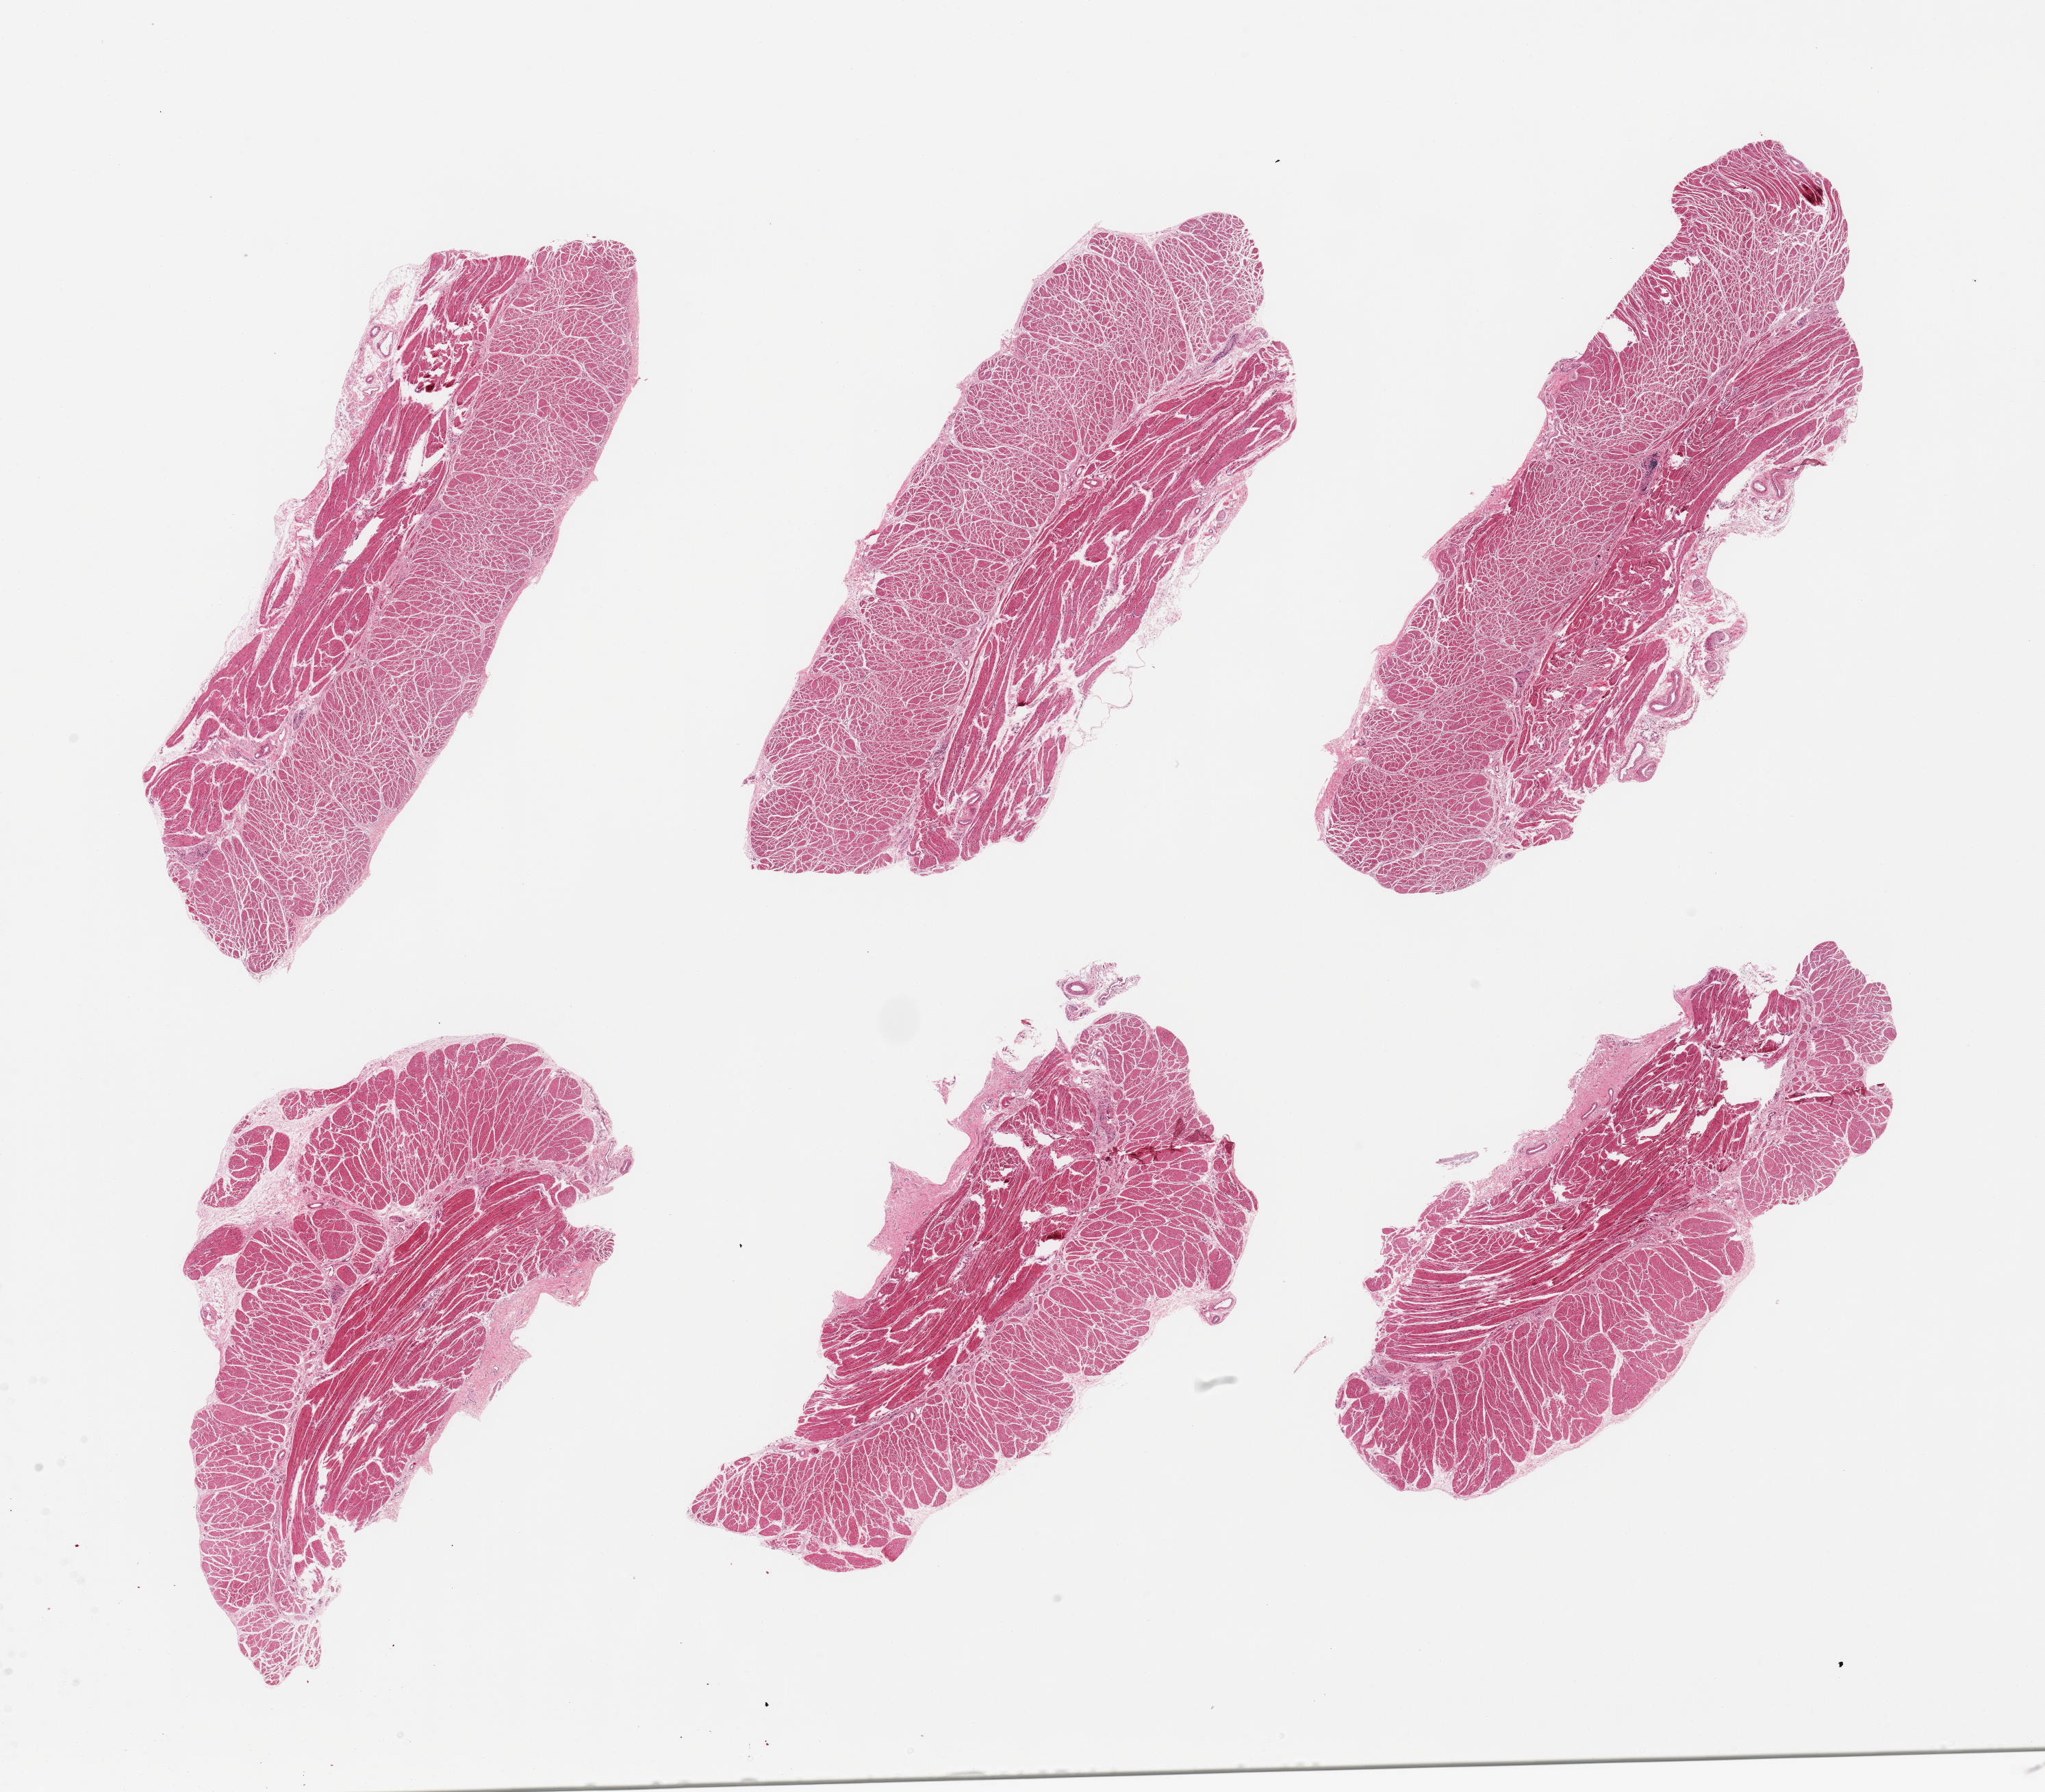
Whole-slide image, H&E stain, brightfield — low-resolution overview of the scanned area, about 23.6 x 20.7 mm, PAXgene-fixed, paraffin-embedded tissue, sampled site (target tissue): gastroesophageal junction, tissue donor sample. Donor sex: female.
Reviewer comment on this tissue sample: 6 pieces; essentially well trimmed target muscularis.